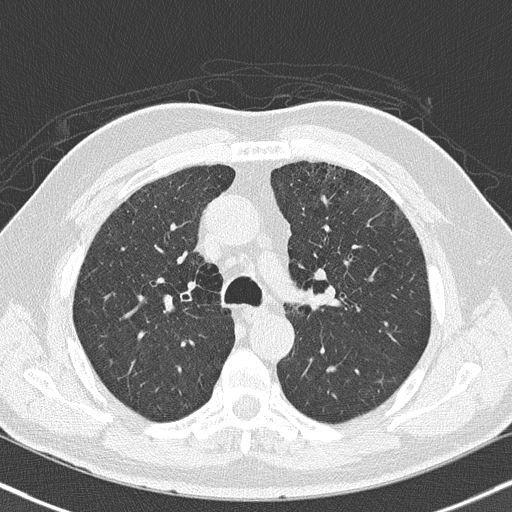
Low-dose screening chest CT, axial slice; second annual screen; lung window (W 1500 / L -600 HU); 2 mm slice thickness; slice 61 of 165 in the series; 512 × 512 image matrix. Male participant, aged 64 years at enrolment. Current smoker at enrolment.
Expert-annotated lung lesion, bounding box (x1, y1, x2, y2) in pixels: (313, 278, 346, 309). Screening reader's record for this exam: no non-calcified nodule ≥4 mm recorded. Official screen result: positive, other. Later outcome: lung cancer diagnosed 72 days after this screen — squamous cell carcinoma, keratinizing, NOS, left upper lobe, moderately differentiated (G2), stage IA (AJCC 6th edition), 4 mm at pathology.